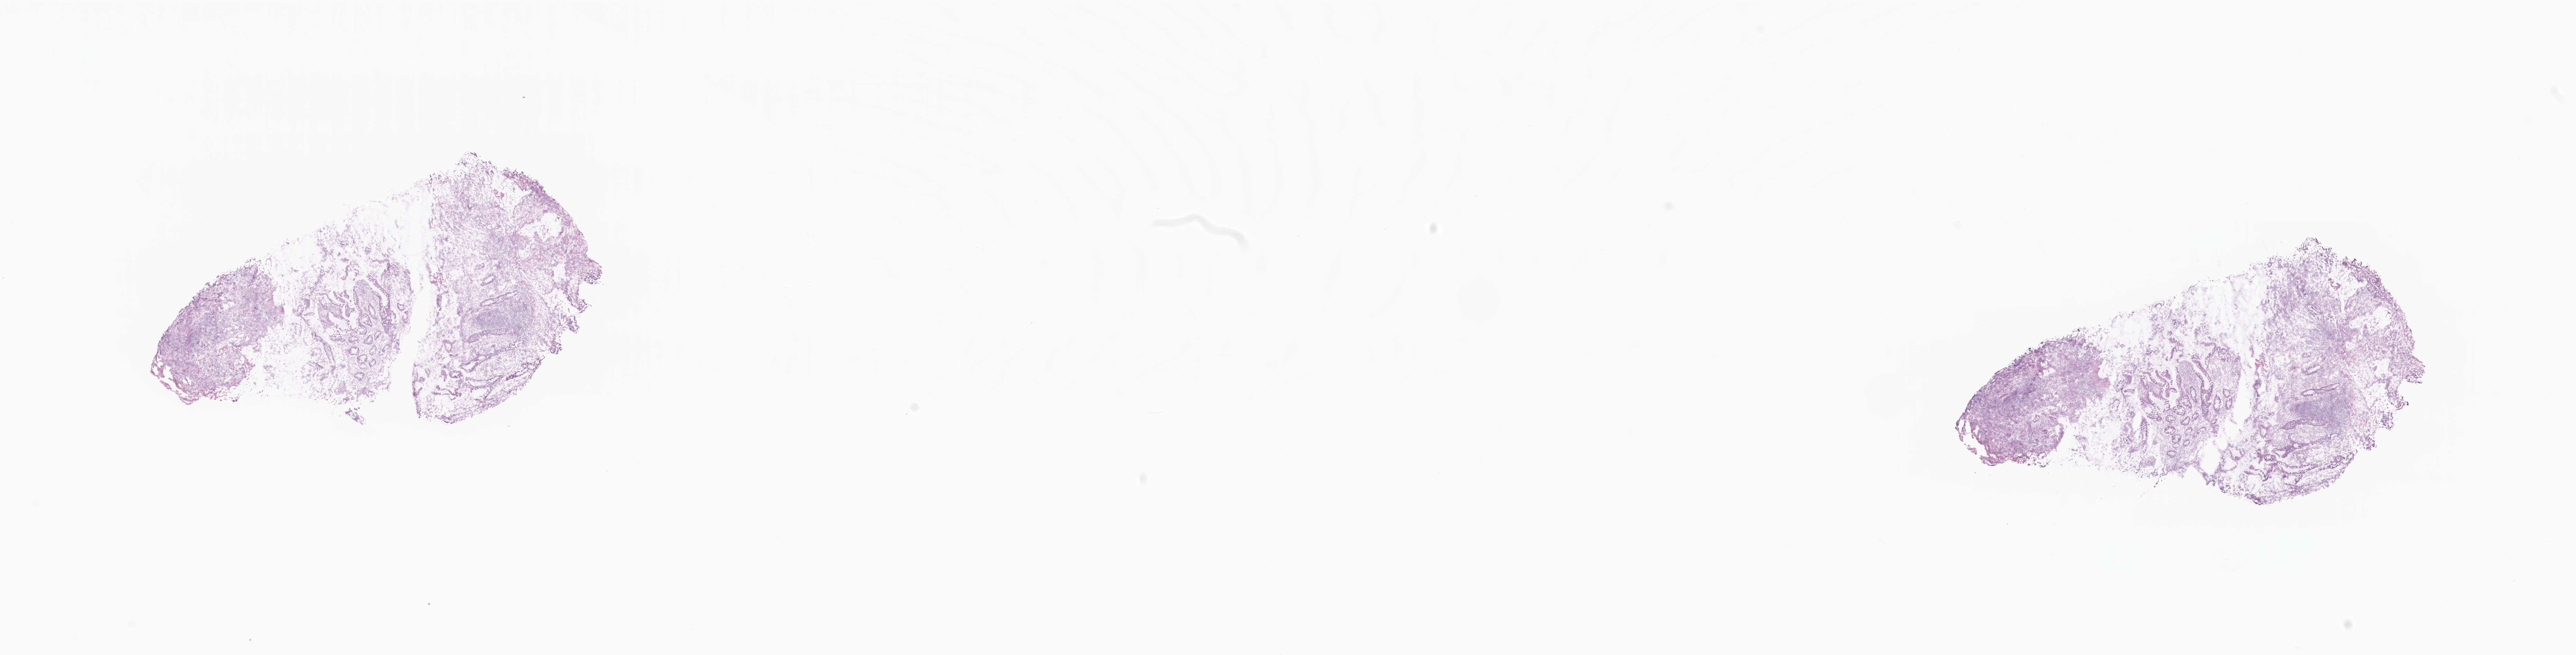
Whole-slide image, hematoxylin and eosin (H&E) stain, a low-resolution overview of the entire scanned area, about 31.4 x 8.0 mm. Cryosection. Primary tumor. Anatomic site: sigmoid colon. Female, age 76 years at initial diagnosis. Composition of this section per pathologist review: tumor cells 48%, tumor nuclei 70%.
Histologic diagnosis: Adenocarcinoma, NOS.